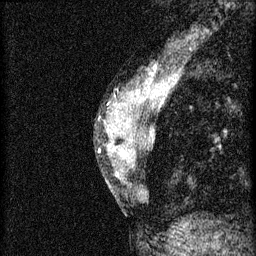
Breast MRI (dynamic contrast-enhanced), one sagittal slice; position 22 of 46 along the scan axis; 3 images stored at this slice position (order not interpretable as contrast timing); 1.5 T; TE 4.2 ms, TR 8.2 ms; 256 × 256 image matrix. Female patient, age 44 years.
Structures marked on this image (semi-automatically segmented with operator editing):
- analysis volume of interest (the breast-tissue region the enhancement analysis was run in; not a lesion): bounding box (x1, y1, x2, y2) in pixels: (110, 128, 153, 181)
- tumour enhancement mask (voxels above the 70 % enhancement threshold inside the analysis volume of interest): (121, 140, 132, 157)